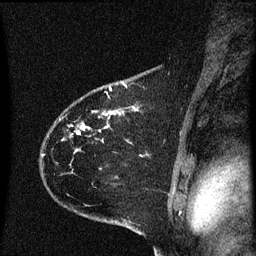
Breast MRI (dynamic contrast-enhanced), one sagittal slice. Position 48 of 60 along the scan axis. Dynamic contrast-enhanced series, image 2 of 3 at this slice position (ordered by acquisition). 1.5 T. TE 4.2 ms, TR 8.4 ms. 256 × 256 image matrix, field of view 200 × 200 mm. Female patient, age 35 years. Case-level facts recorded for this patient, not image findings: setting: breast cancer imaged before/during neoadjuvant chemotherapy; receptor status: HER2-positive.
Outlined on this slice (semi-automatically segmented with operator editing):
- analysis volume of interest (the breast-tissue region the enhancement analysis was run in; not a lesion): bounding box (x1, y1, x2, y2) in pixels: (43, 68, 174, 173)
- tumour enhancement mask (voxels above the 70 % enhancement threshold inside the analysis volume of interest): (77, 86, 127, 133)